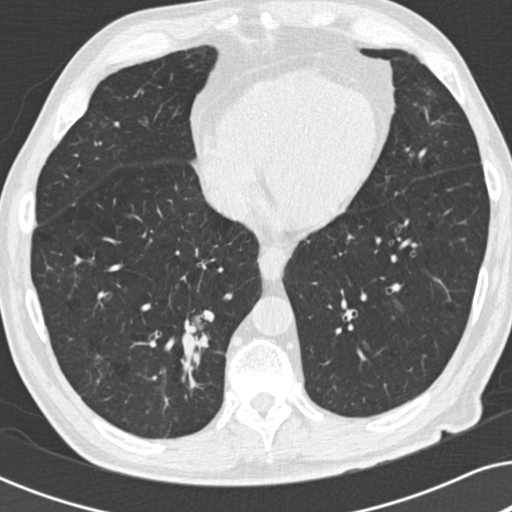
Low-dose screening chest CT, one axial slice; position 79 of 191 along the scan axis; 120 kVp; lung window (W 1500 / L -600 HU); 2 mm slice thickness; 512 × 512 image matrix, field of view 330 × 330 mm.
Structures marked on this image (expert manual segmentation):
- lesion 1 (tumor, lower lobe of right lung): bounding box <181,313,209,348> (left, top, right, bottom; pixels)